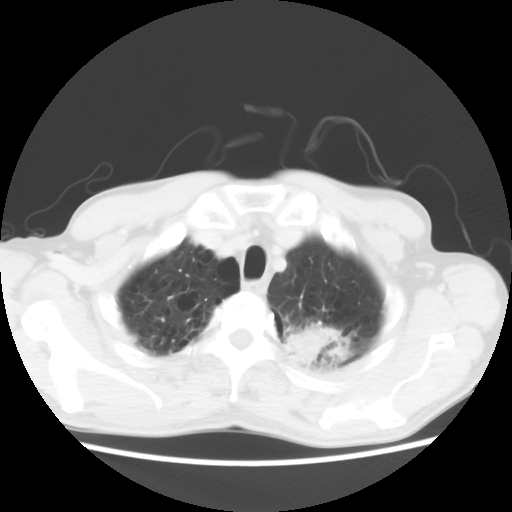
Chest CT, one axial slice. Position 56 of 64 along the scan axis. Reconstruction kernel STANDARD. 120 kVp. Lung window (W 1500 / L -600 HU). 5 mm slice thickness. 512 × 512 image matrix, field of view 346 × 346 mm. Patient: male, 63 years. From the clinical record (not read from this slice): clinical TNM (as recorded): T2 N0 M0.
Annotated regions visible in this slice (bounding box drawn by a radiologist):
- lung tumour (recorded histology: adenocarcinoma): bounding box [x1, y1, x2, y2] px = [284, 320, 348, 380]